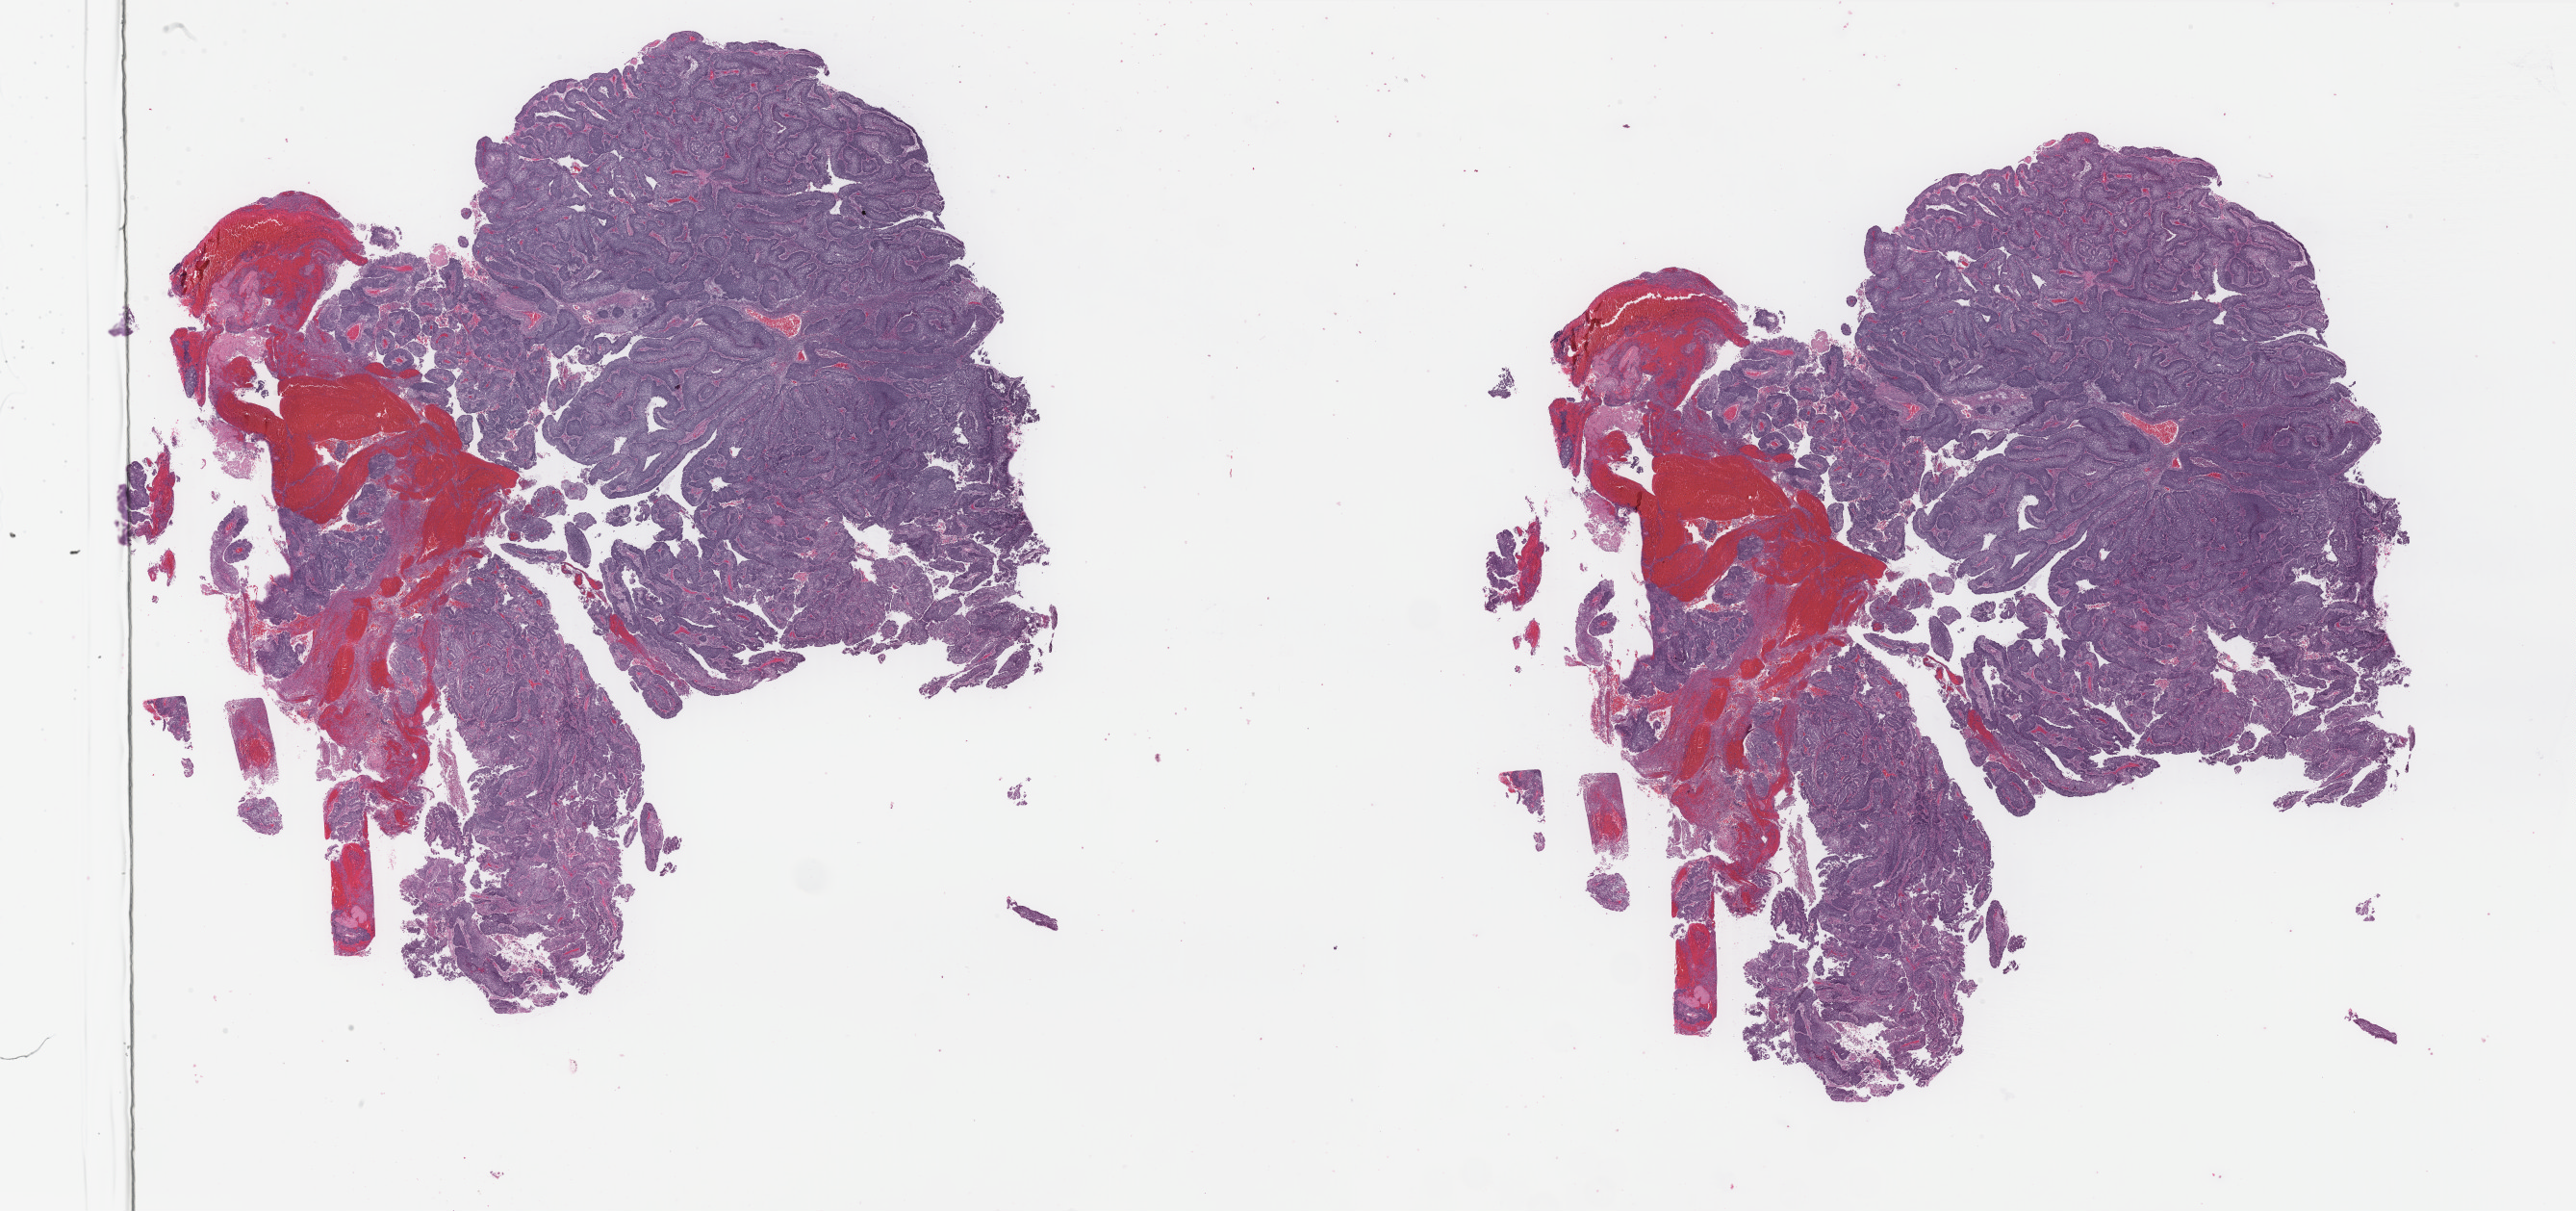
H&E-stained whole-slide image, low-resolution overview of the scanned area, about 42.4 x 19.9 mm; formalin-fixed paraffin-embedded (FFPE) diagnostic section; sample: primary tumour, uterus. Patient: female, age at initial diagnosis 72 years. Histologic grade: G3 (poorly differentiated).
Histologic diagnosis: Endometrioid adenocarcinoma, NOS (endometrium). FIGO stage: IB.